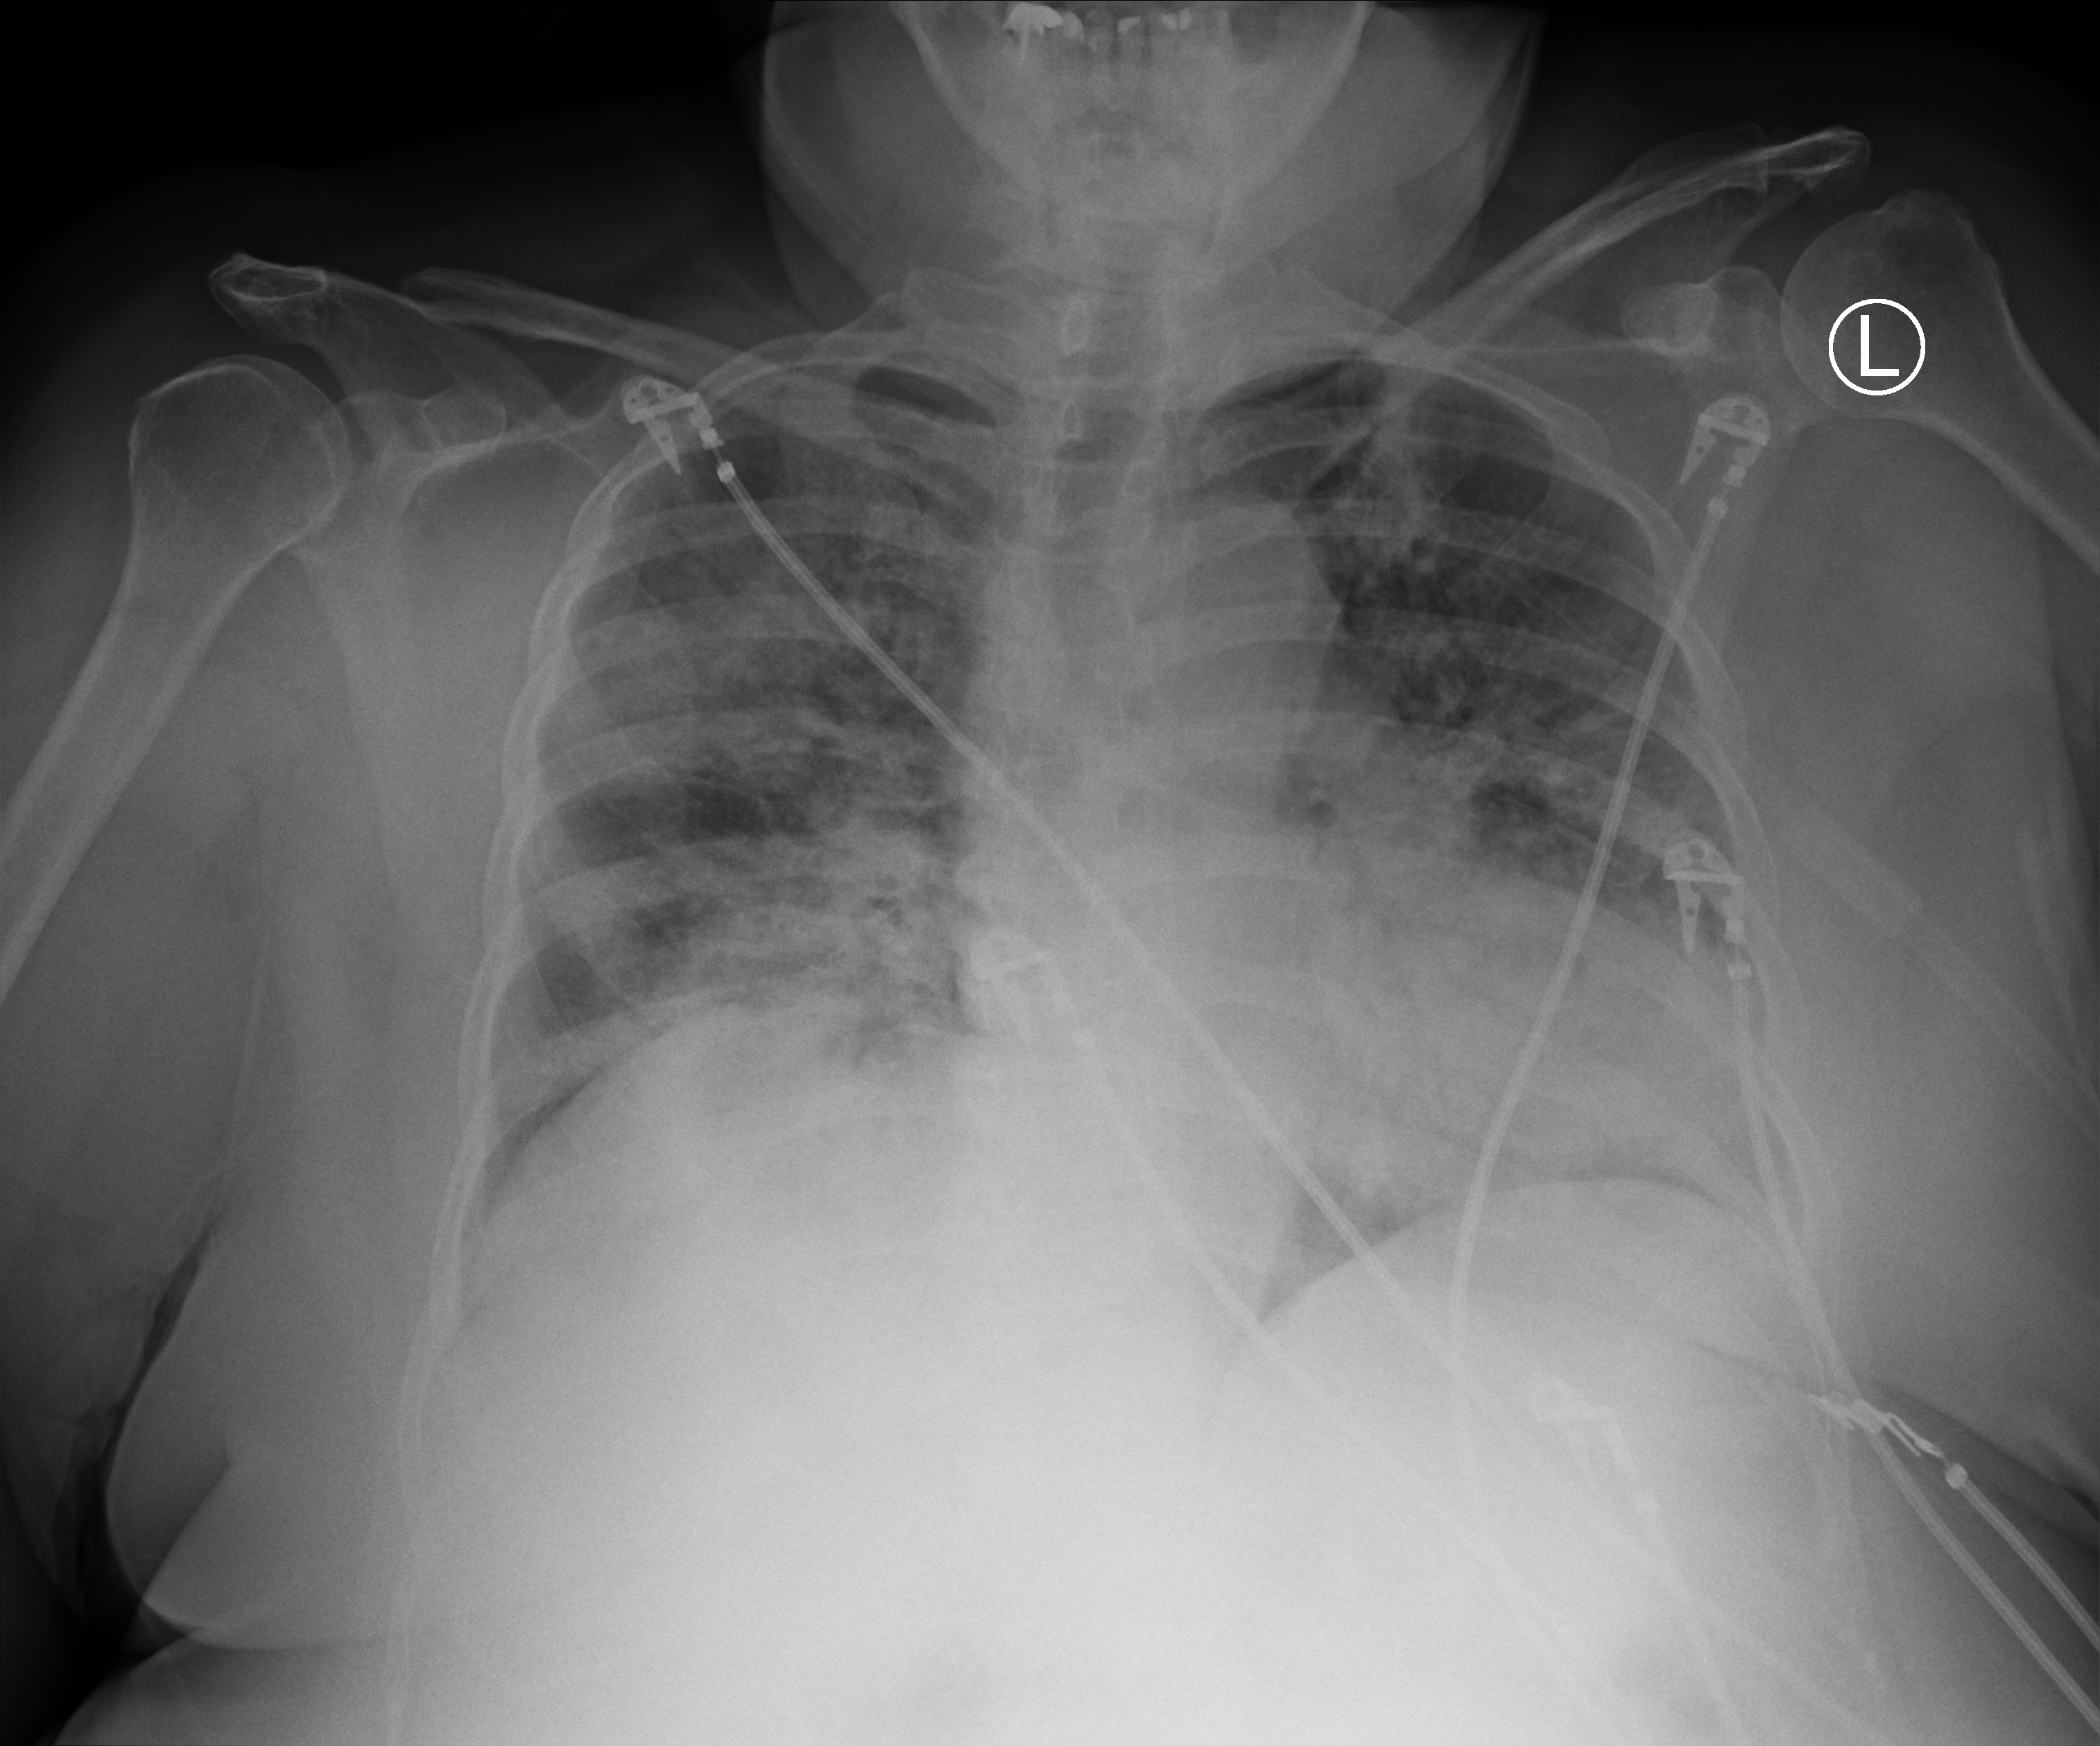
Chest X-ray (portable), anteroposterior (AP) projection. Patient hospitalised with COVID-19; female, aged 60–74 years.
Admission-level facts for this patient (not findings on this image; timing relative to this image not recorded): chronic kidney disease (admission record): no.